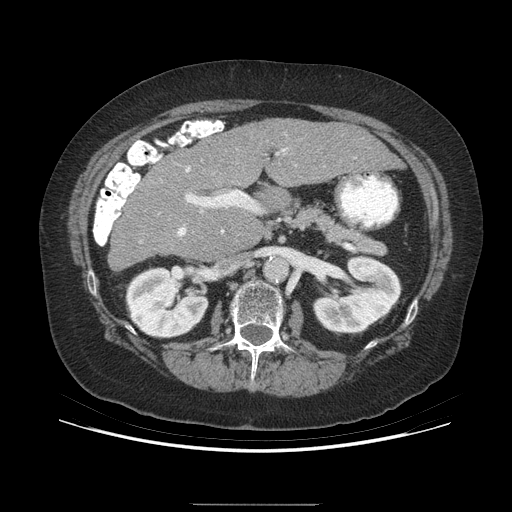
Contrast-enhanced abdominal CT (liver protocol), one axial slice; slice 146 of 192 in the series (ordered by position); reconstruction kernel STANDARD; soft-tissue window (W 400 / L 40 HU); 2.5 mm slice thickness; 512 × 512 image matrix. Case-level facts recorded for this patient, not image findings: diagnosis: hepatocellular carcinoma (patient treated with transarterial chemoembolisation; whether this scan precedes or follows treatment is not stated here); TNM stage (as recorded): Stage-I; Child-Pugh class: A; tumour differentiation: moderately differentiated; tumour nodularity: uninodular.
Outlined on this slice (semi-automatically segmented with operator editing):
- liver parenchyma outside the tumour (the mass and vessels are separate outlines, so this box may not span the whole liver): bounding box [x1, y1, x2, y2] px = [108, 118, 400, 268]
- liver vessels: [177, 148, 286, 236]